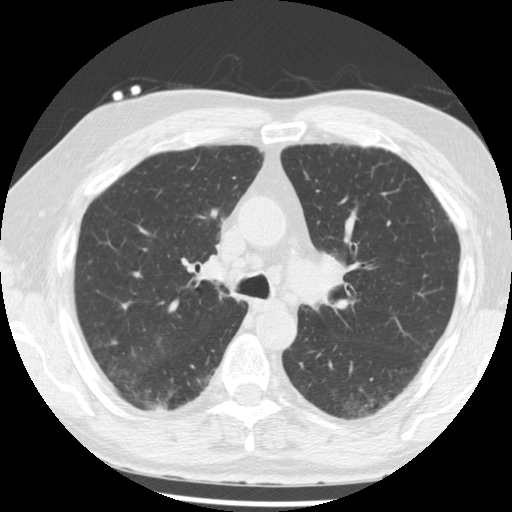
Low-dose screening chest CT, one axial slice; slice 139 of 221 in the series (ordered by position); lung window (W 1500 / L -600 HU); 2.5 mm slice thickness; 512 × 512 image matrix.
Structures marked on this image (outlined manually by an expert reader):
- lesion 1 (tumor, lower lobe of right lung): box from (x=149, y=406) to (x=175, y=413) px